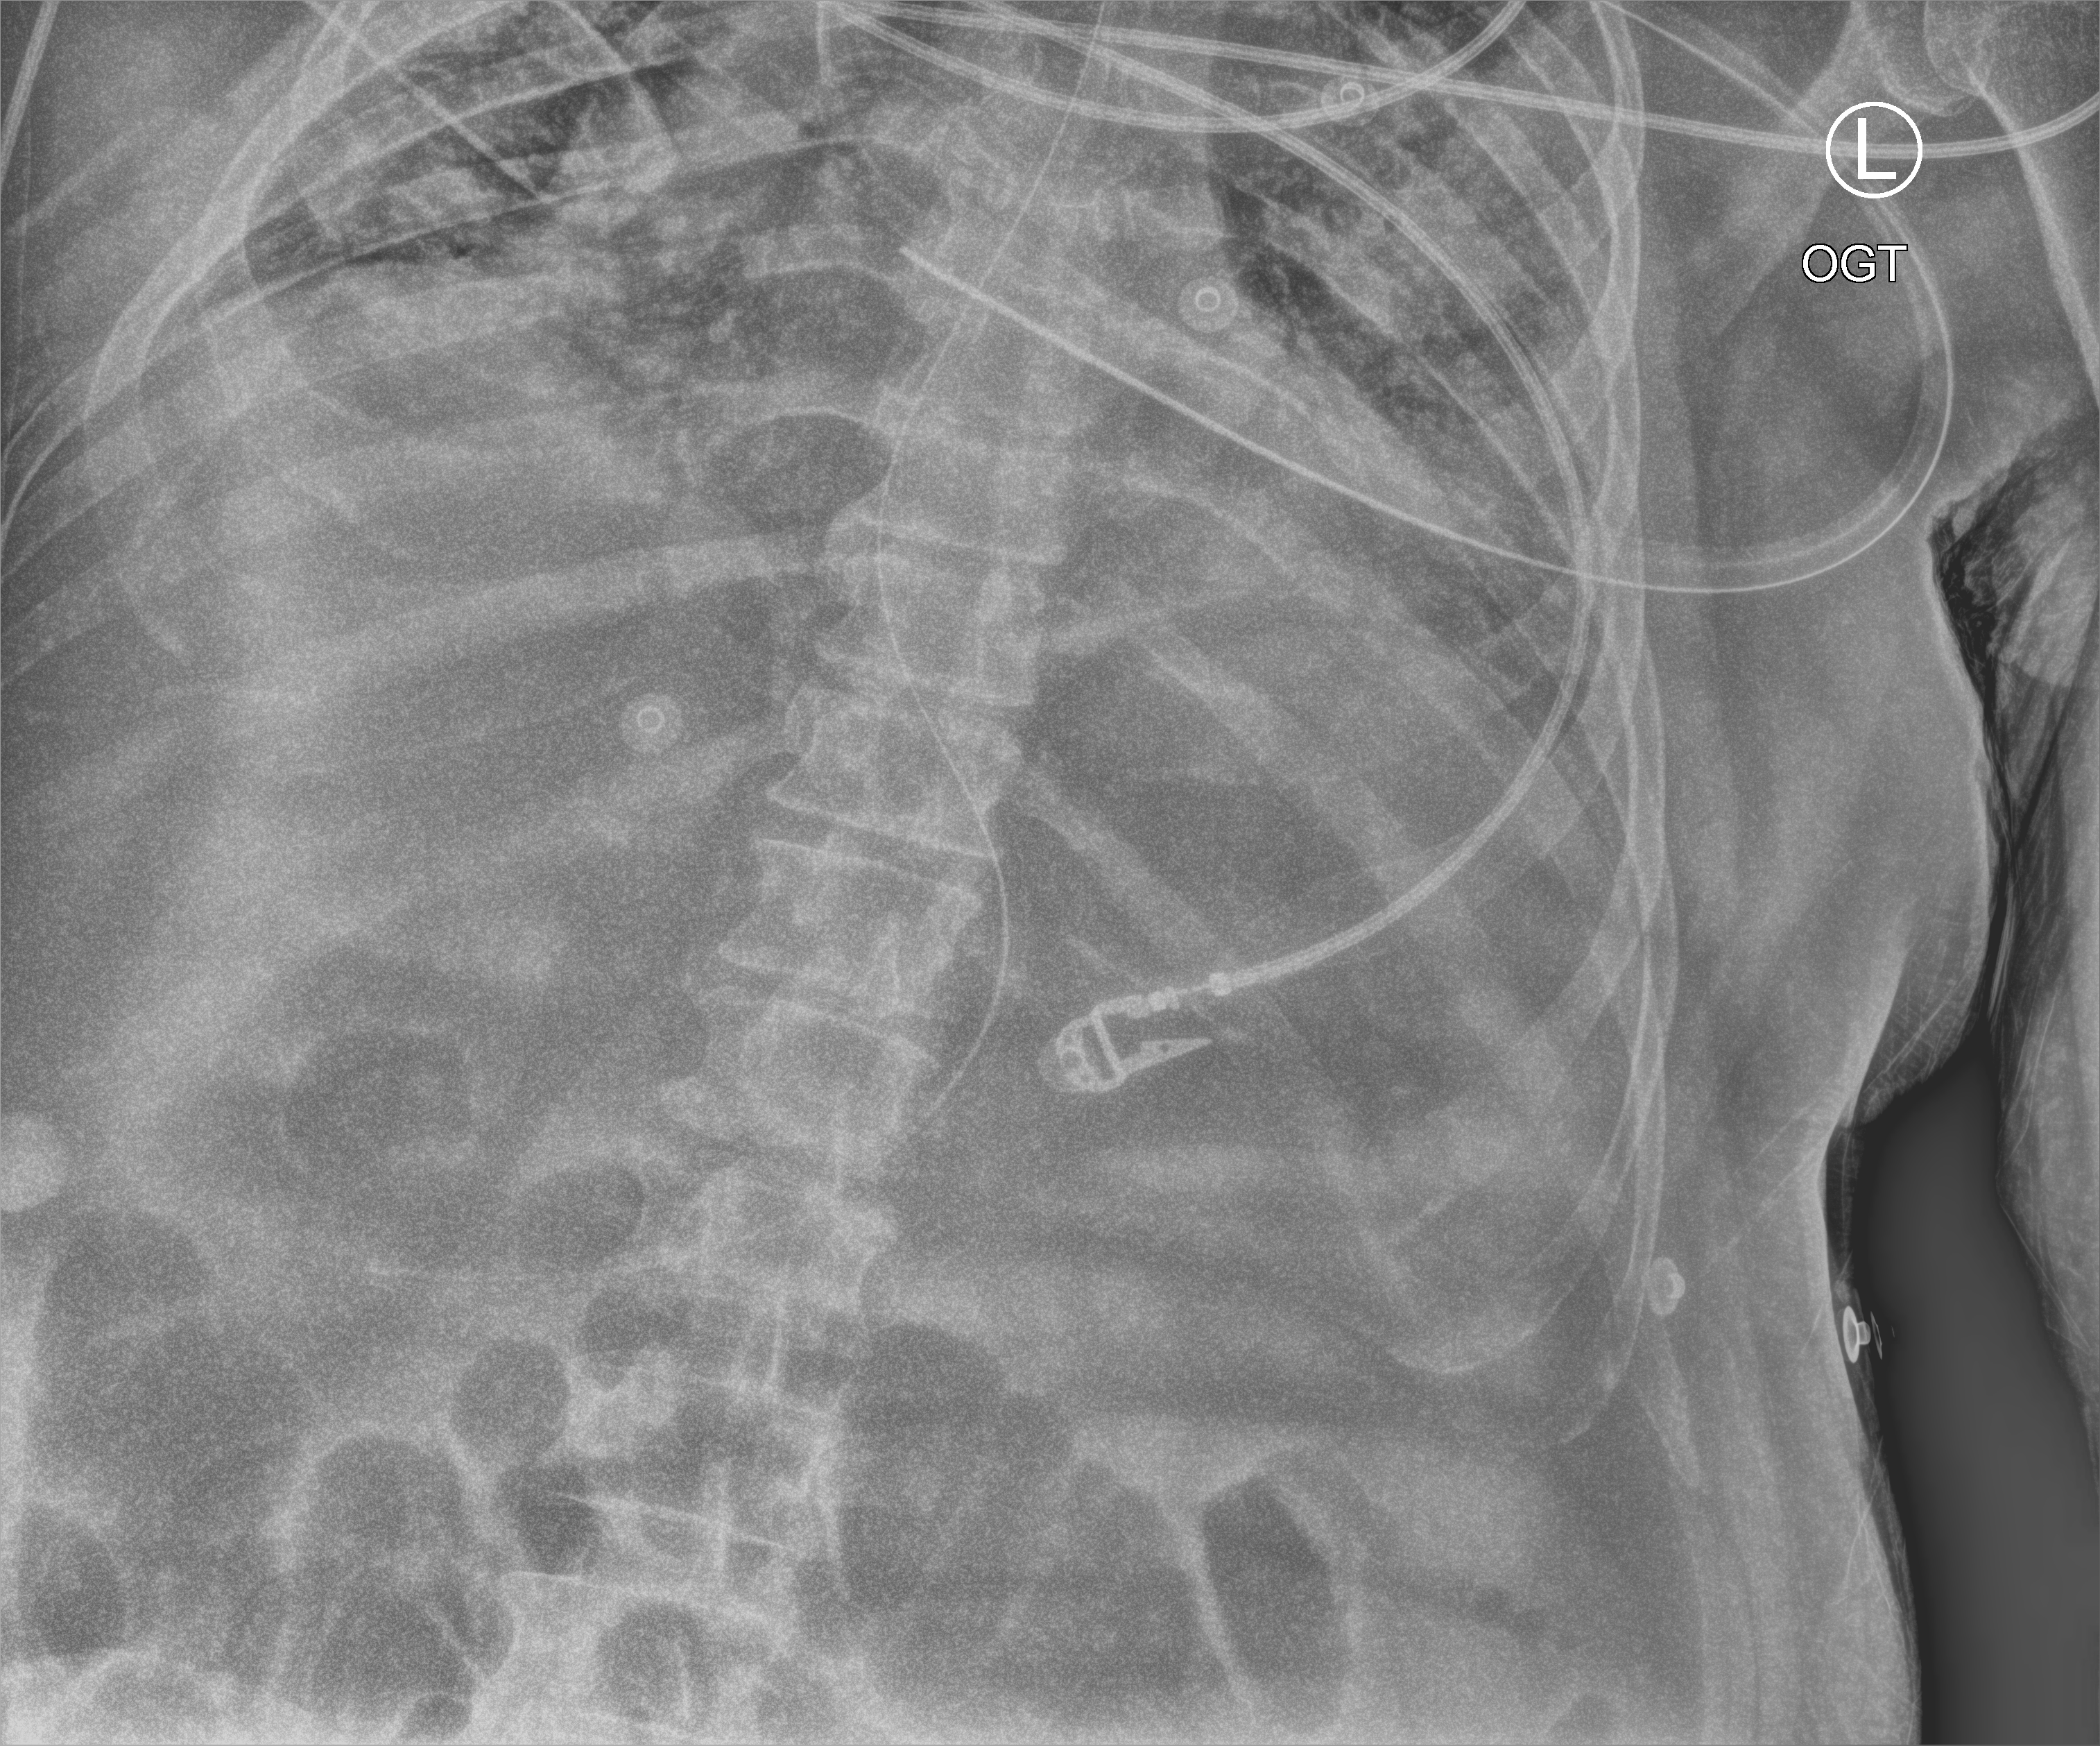
Portable chest radiograph, anteroposterior (AP) projection. Male patient hospitalised with COVID-19, age 18–59 years.
Admission-level facts for this patient (not findings on this image; timing relative to this image not recorded): admitted to intensive care during this hospital stay: yes; hypertension (admission record): yes; COPD (admission record): no.